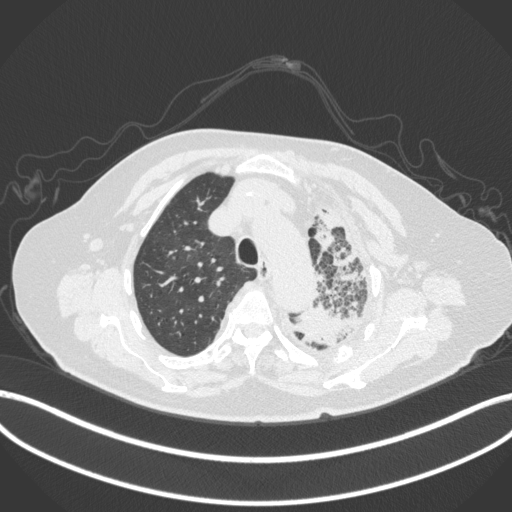
Chest CT, one axial slice; position 305 of 399 along the scan axis; 120 kVp; lung window (W 1500 / L -600 HU); 1 mm slice thickness; 512 × 512 image matrix, field of view 400 × 400 mm. Patient: female, 75 years. Case-level facts recorded for this patient, not image findings: clinical TNM (as recorded): T3 N3 M1.
Outlined on this slice (rectangle marked by the reading radiologist):
- lung tumour (recorded histology: adenocarcinoma): bounding box [x1, y1, x2, y2] px = [293, 303, 356, 346]